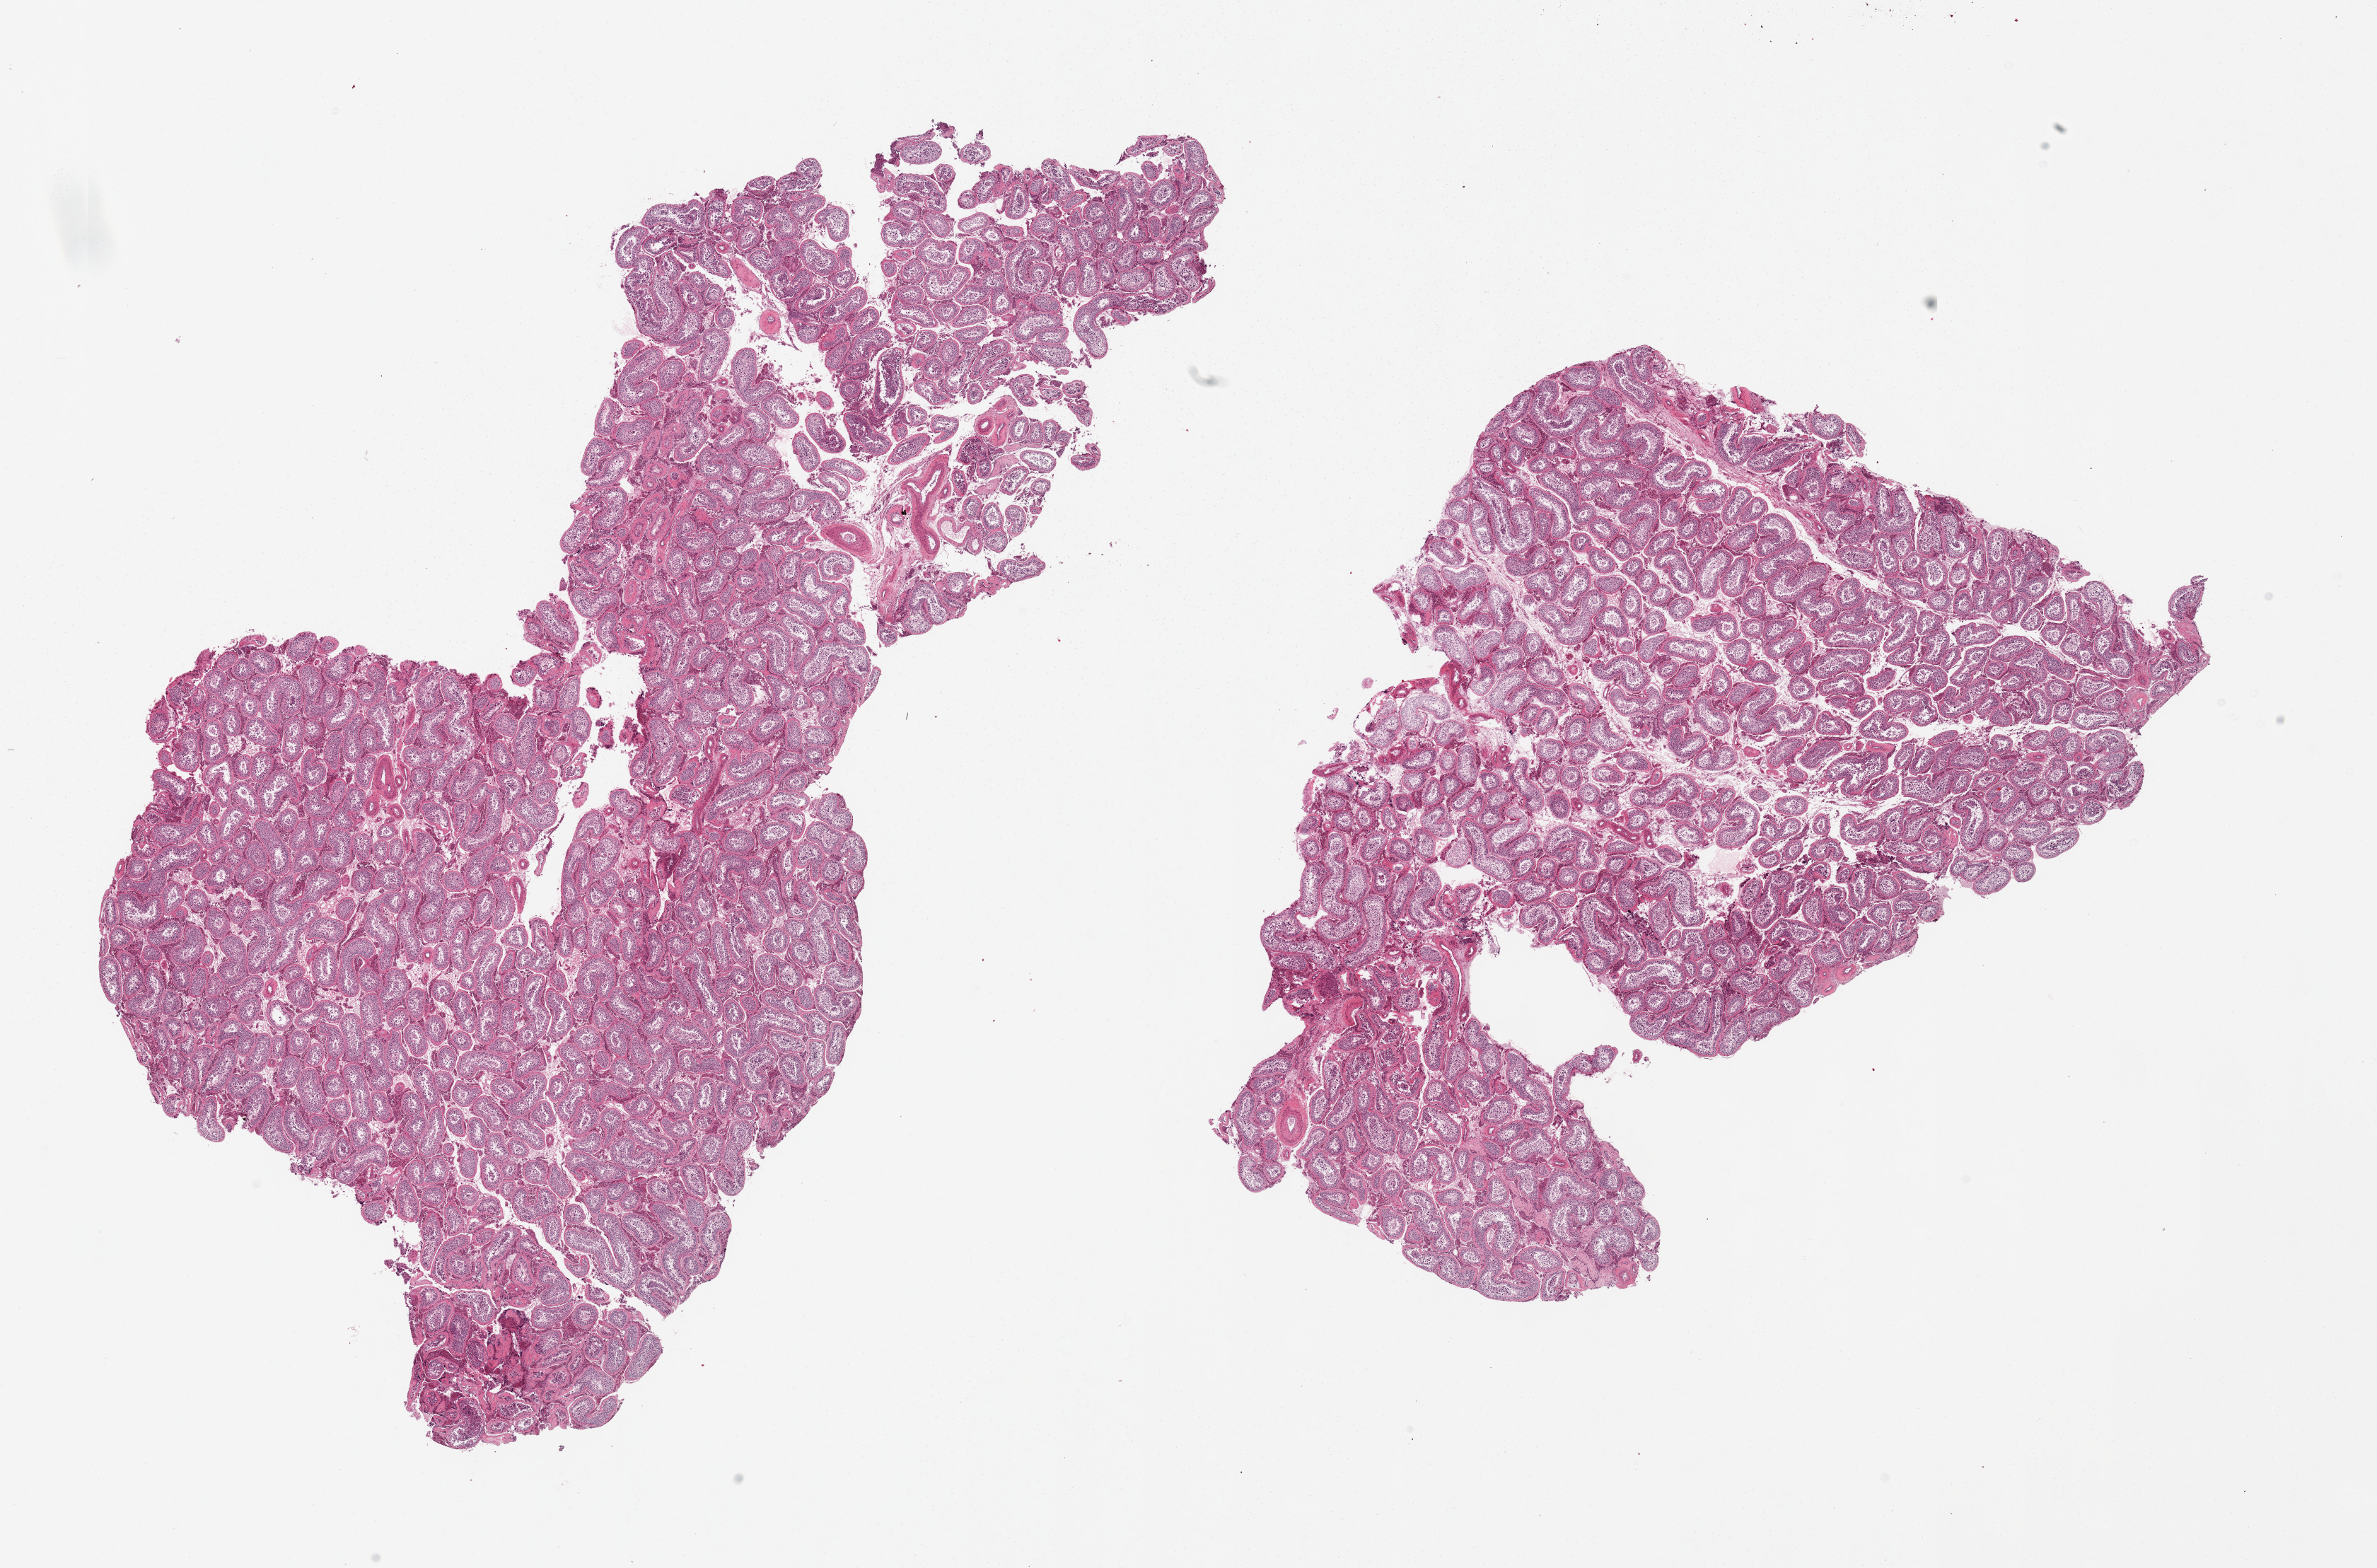
Hematoxylin and eosin (H&E) whole-slide image — shown as a low-resolution overview of the whole scanned area (about 26.6 x 17.5 mm, acquisition: 20x scan); PAXgene-fixed paraffin-embedded (PFPE) section; section of testis (target tissue); tissue donor sample. Male donor.
Pathologist's review note for this sample: 2 pieces; spermatogenesis.